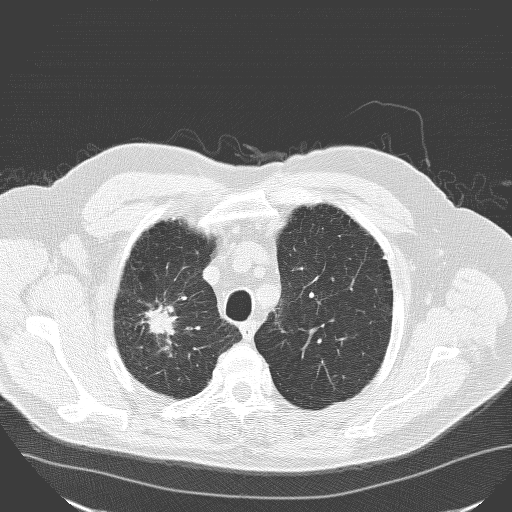
Axial slice from a low-dose chest CT screening exam; baseline screening round; lung window (W 1500 / L -600 HU); 3.2 mm slice thickness. Male participant, aged 71 years at enrolment. Current smoker at enrolment.
Lesion marked by an expert reader, bounding box (x1, y1, x2, y2) in pixels: (115, 279, 189, 355). Reader record for this screening exam (exam-level; its link to the box is not recorded): non-calcified nodule or mass ≥4 mm, right upper lobe, 30 × 25 mm, spiculated (stellate) margins, soft tissue attenuation. Official screen result: positive, change unspecified: nodule(s) >= 4 mm or enlarging nodule(s), mass(es), or other non-specific abnormalities suspicious for lung cancer. Participant outcome: lung cancer diagnosed 182 days after this screen — squamous cell carcinoma, NOS, right upper lobe, poorly differentiated (G3), stage IA (AJCC 6th edition), 30 mm at pathology.